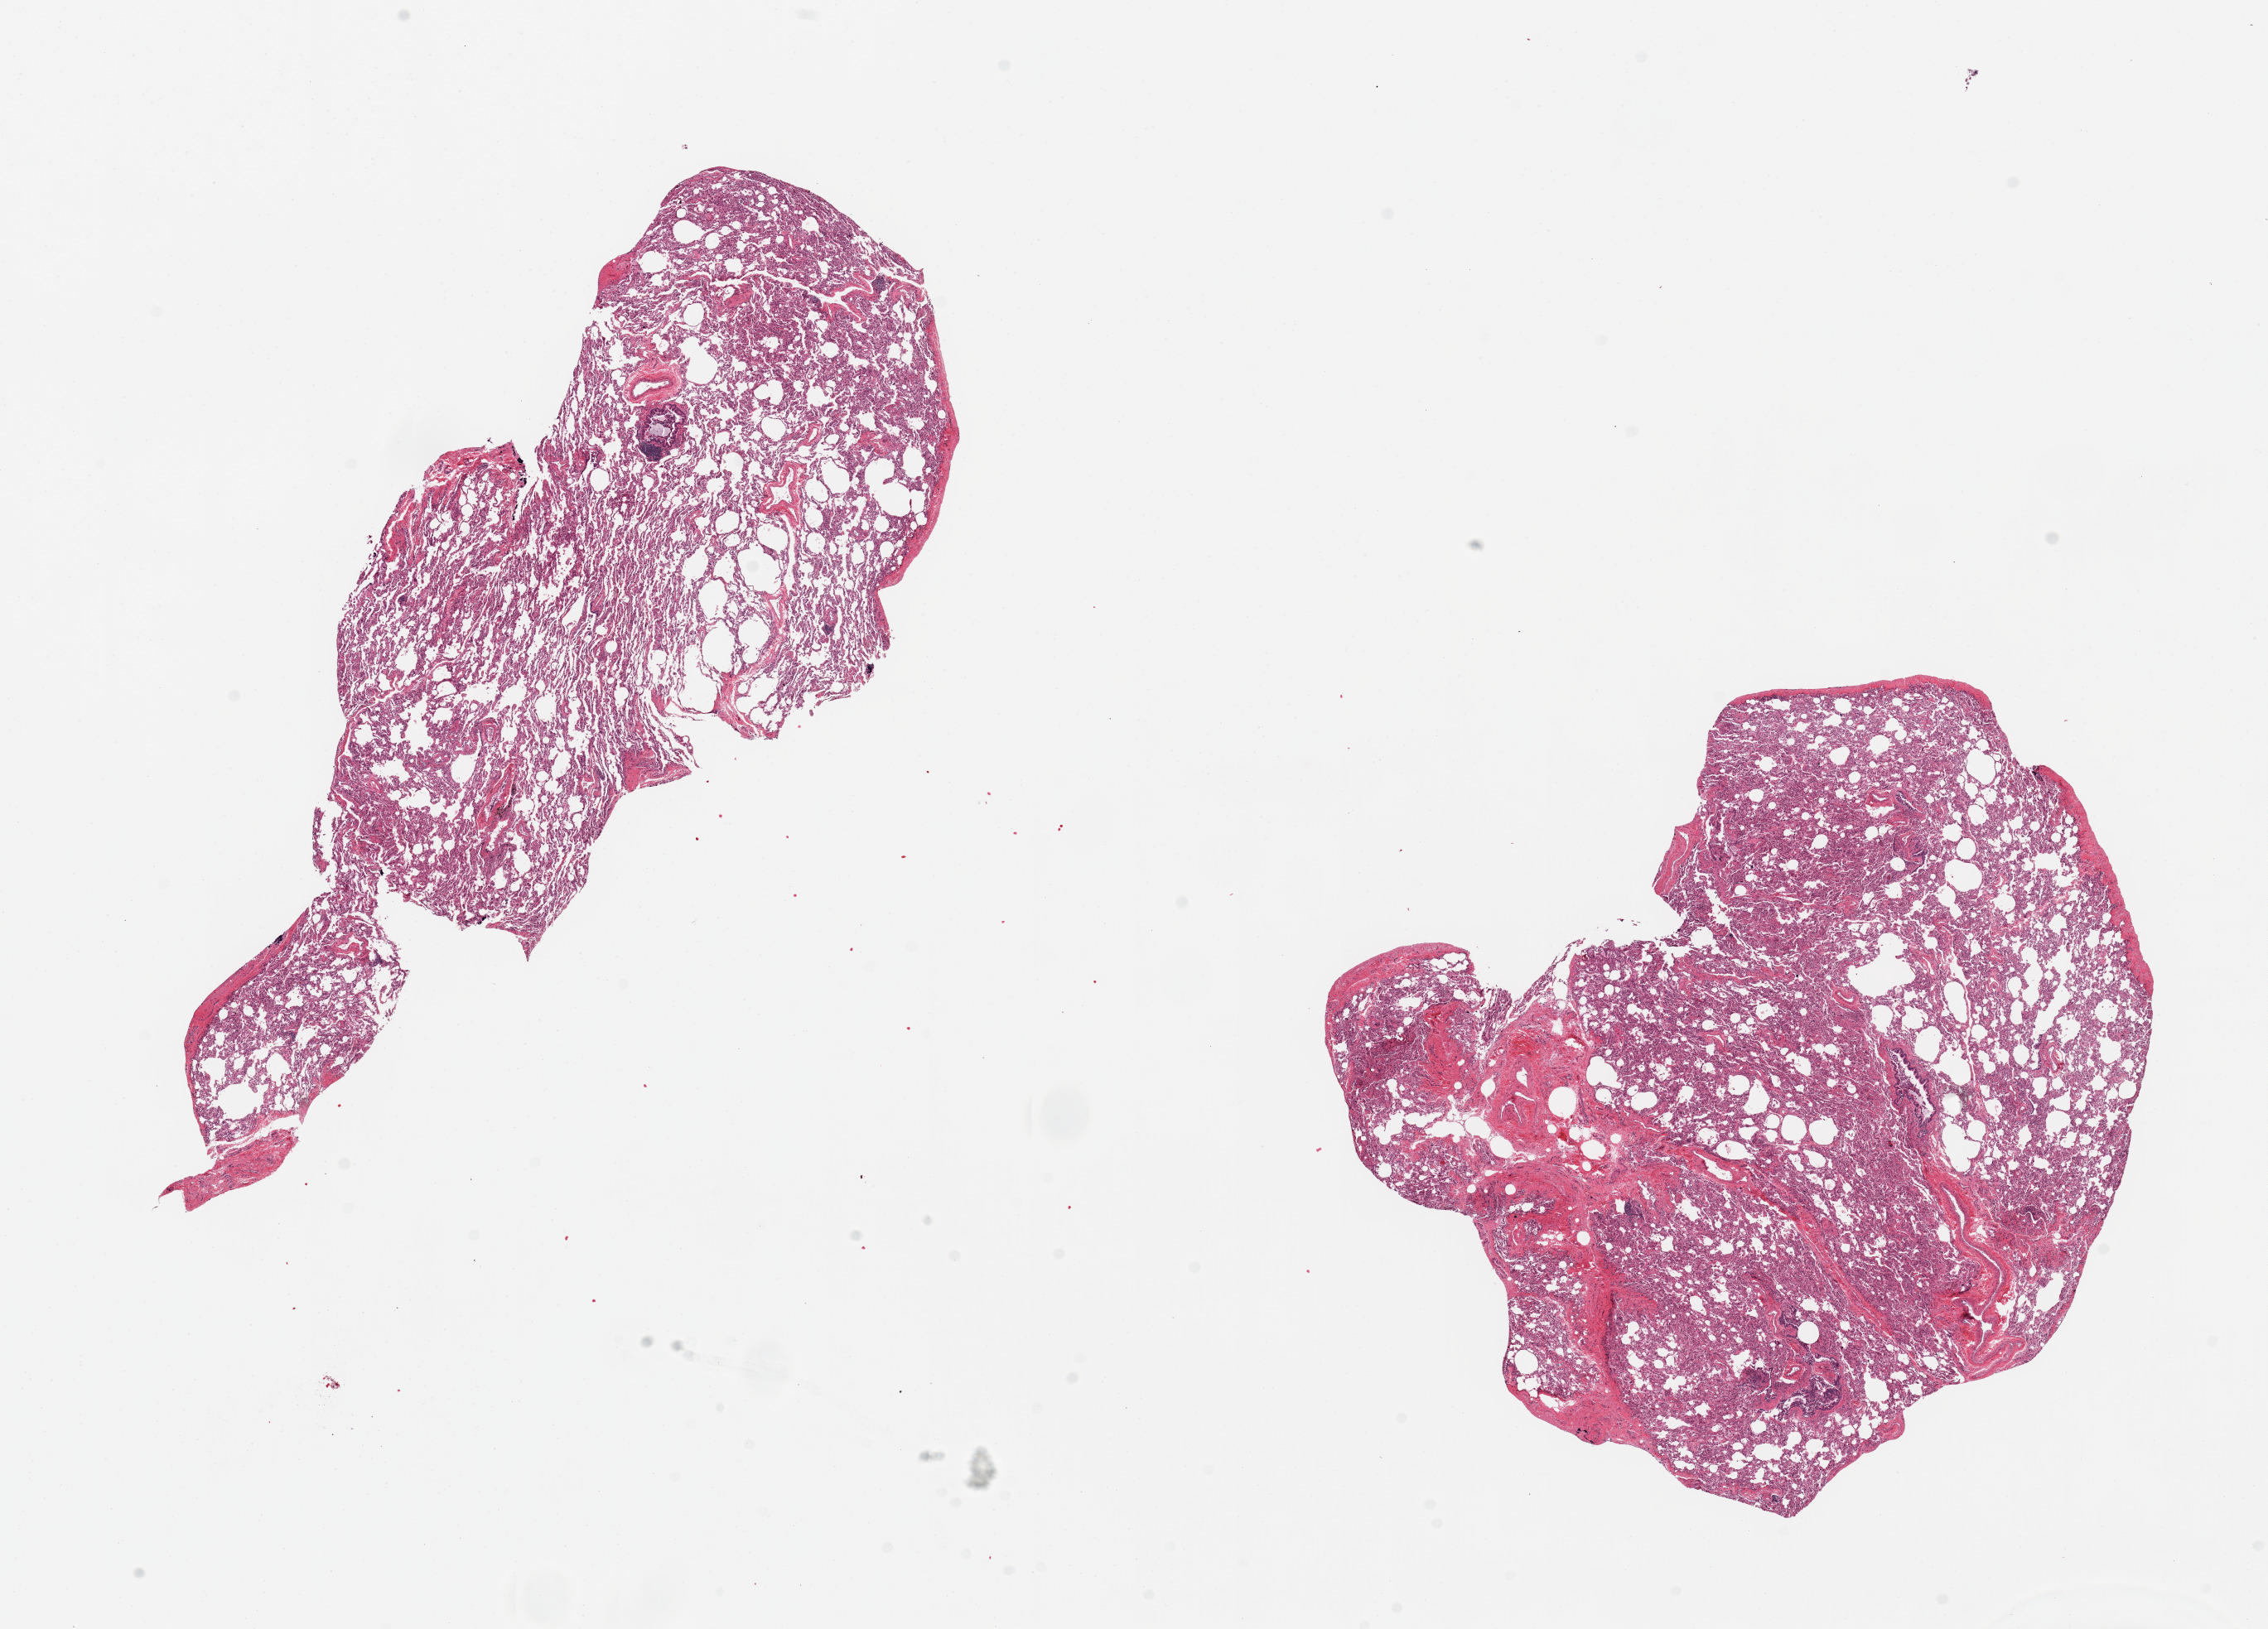
Whole-slide image, haematoxylin and eosin stain, brightfield — low-resolution overview of the scanned area, about 21.7 x 15.6 mm (acquisition: 20x scan). PAXgene-fixed, paraffin-embedded tissue. Target tissue: lung. Donor tissue sample. Female donor.
Review note (as recorded): 2 pieces; pleura is present (target is 1cm below pleura), some atelectasis.